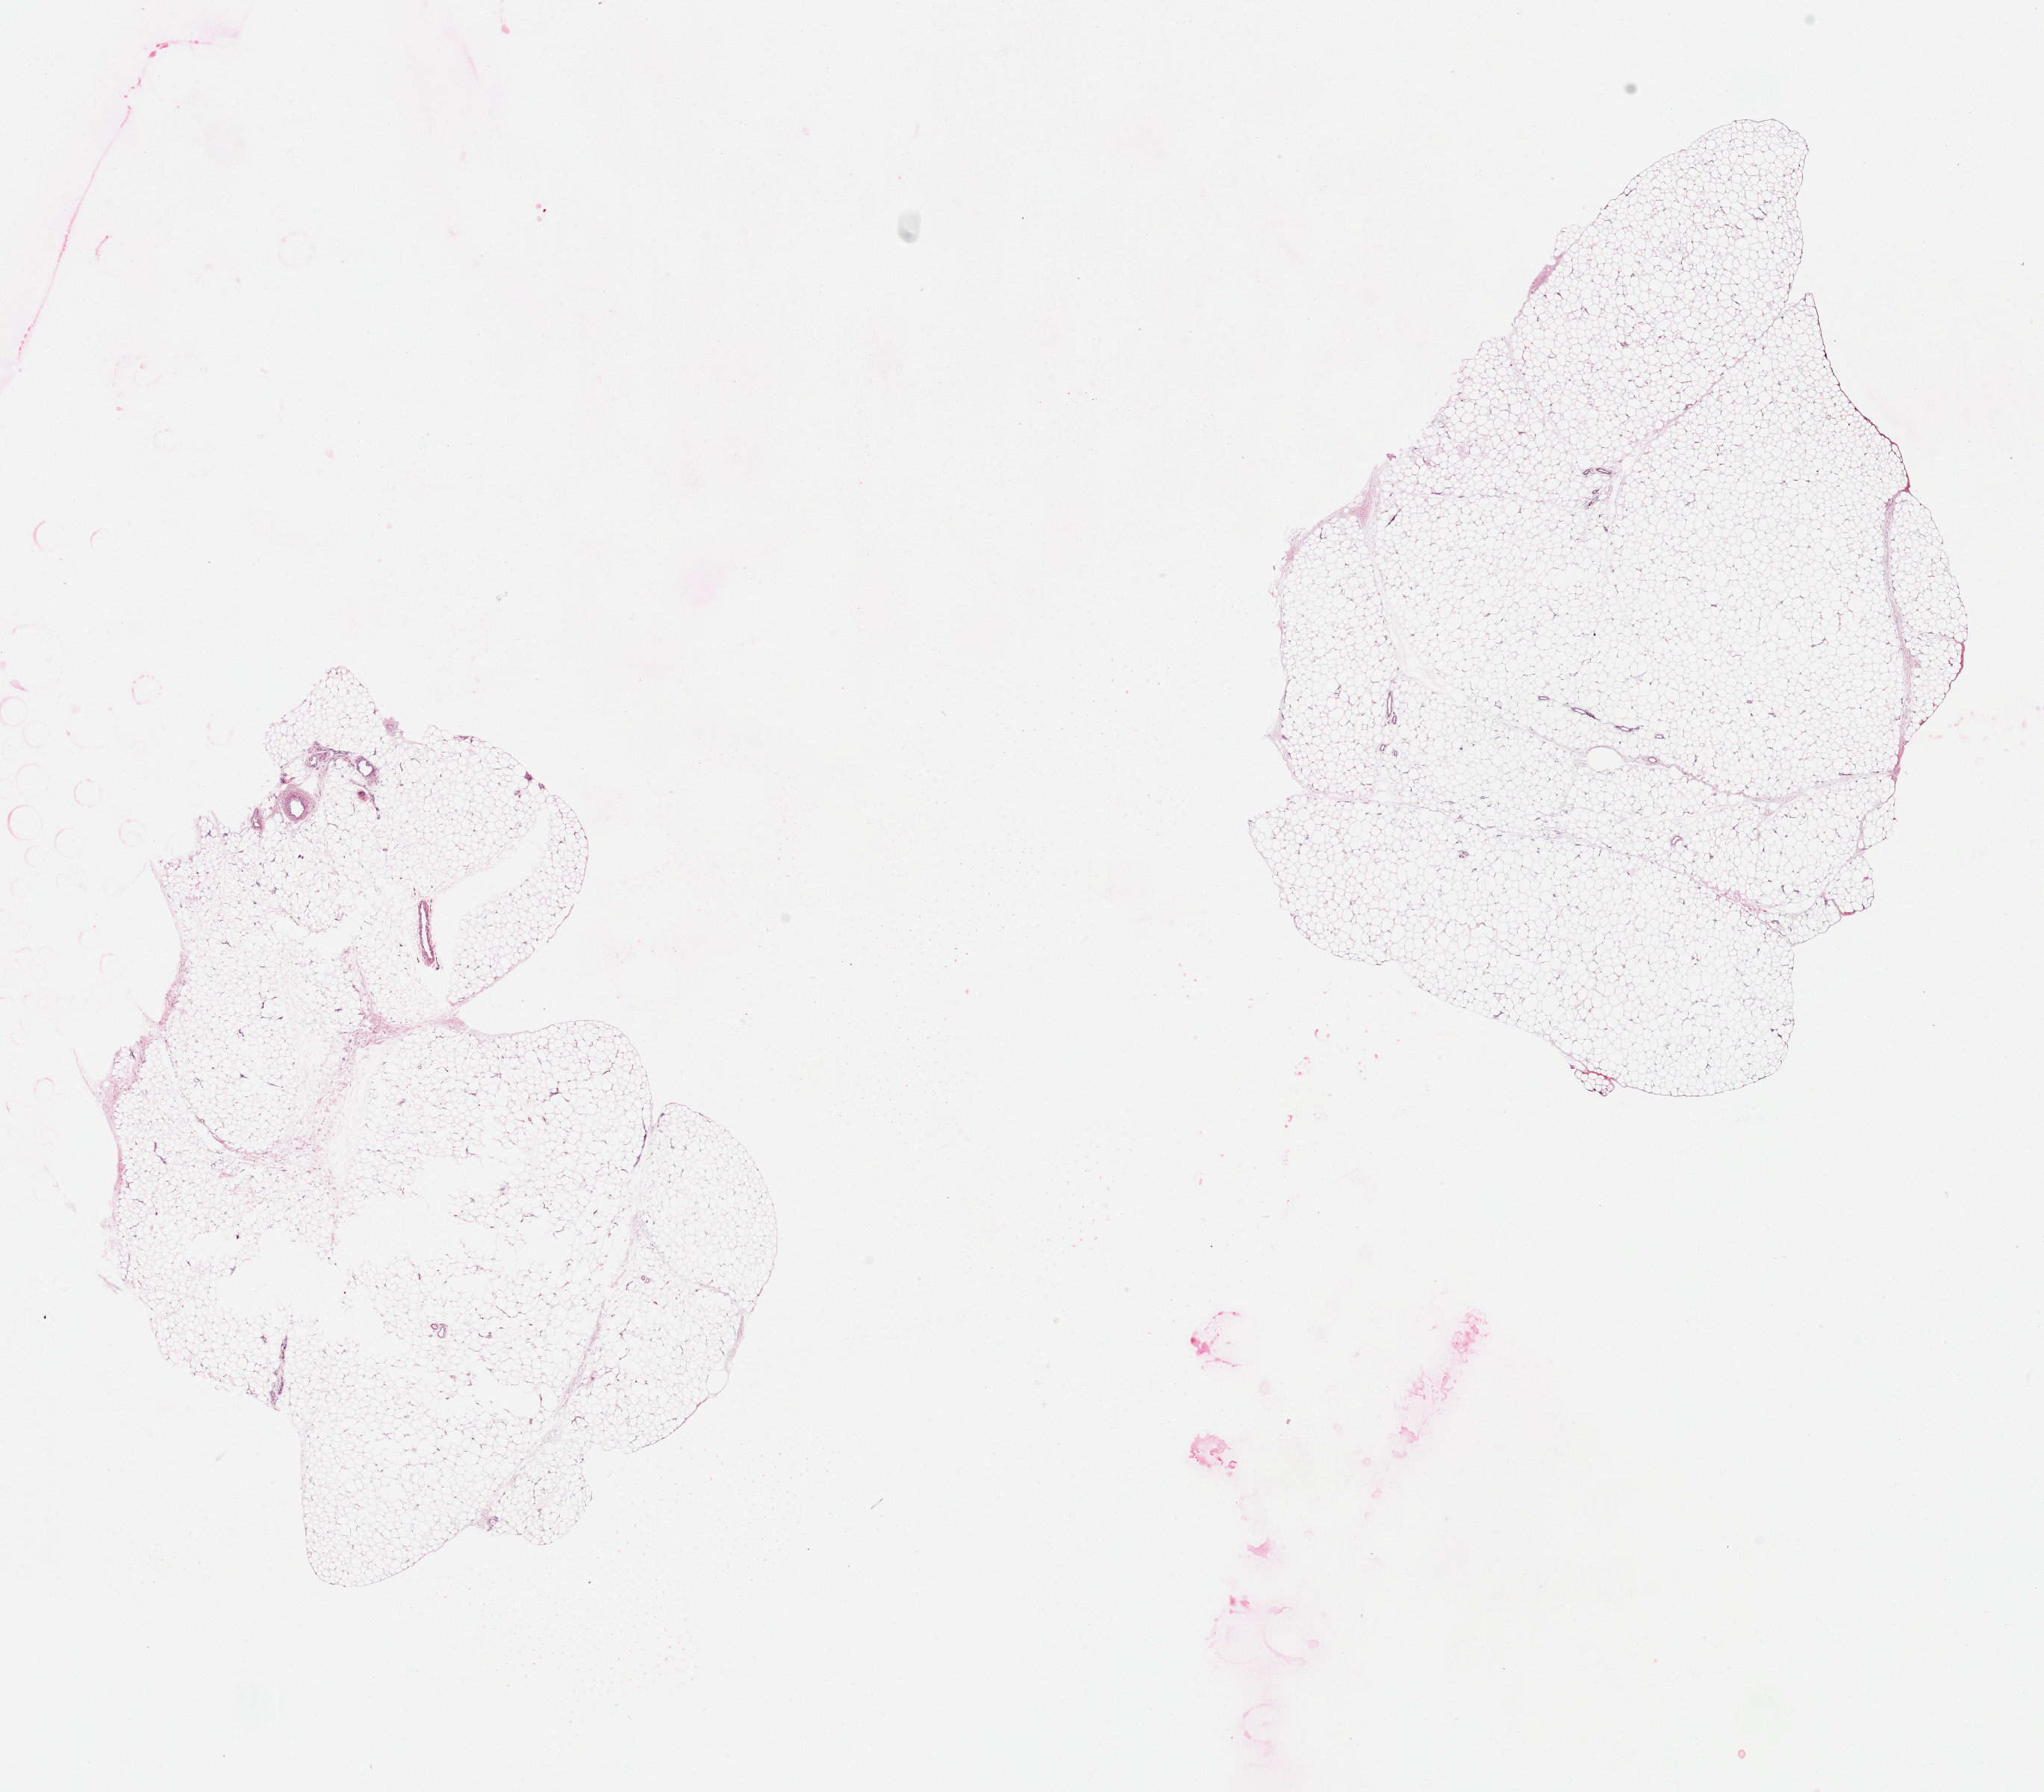
Whole-slide image, haematoxylin and eosin stain, low-resolution overview of the scanned area, about 21.7 x 19.0 mm (acquisition: 20x scan), PAXgene-fixed, paraffin-embedded tissue, target tissue: adipose tissue, donor tissue sample. Donor: female.
Reviewer comment on this tissue sample: 2 pieces.